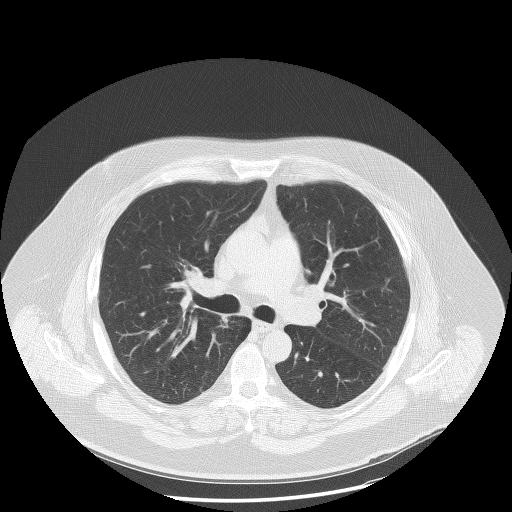
Axial slice from a low-dose chest CT screening exam. Second screening round (one year after baseline). Lung window (W 1500 / L -600 HU). Lung (sharp) reconstruction kernel (BONE). Slice 48 of 132 in the series. 512 × 512 image matrix, field of view 430 × 430 mm. Male, age 58 years at enrolment. Former smoker at enrolment.
Lesion marked by an expert reader, bounding box <208,305,242,348> (left, top, right, bottom; pixels). No non-calcified nodule or mass ≥4 mm was recorded by the screening reader at this exam. Lung cancer was diagnosed 471 days after this screen (after the third annual screen): squamous cell carcinoma, NOS, right upper lobe, moderately differentiated (G2), stage IA (AJCC 6th edition), 18 mm at pathology.